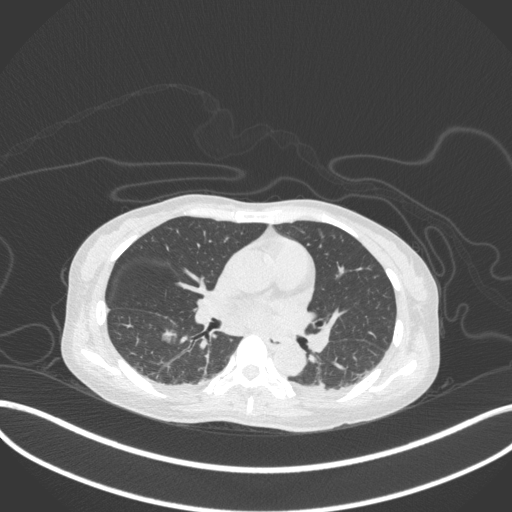
Chest CT, one axial slice; position 161 of 260 along the scan axis; 120 kVp; lung window (W 1500 / L -600 HU); 1 mm slice thickness; 512 × 512 image matrix. Patient: female, 44 years. Case-level facts recorded for this patient, not image findings: clinical TNM (as recorded): T1c N0 M0.
Outlined on this slice (bounding box drawn by a radiologist):
- lung tumour (recorded histology: adenocarcinoma): box from (x=160, y=321) to (x=179, y=347) px